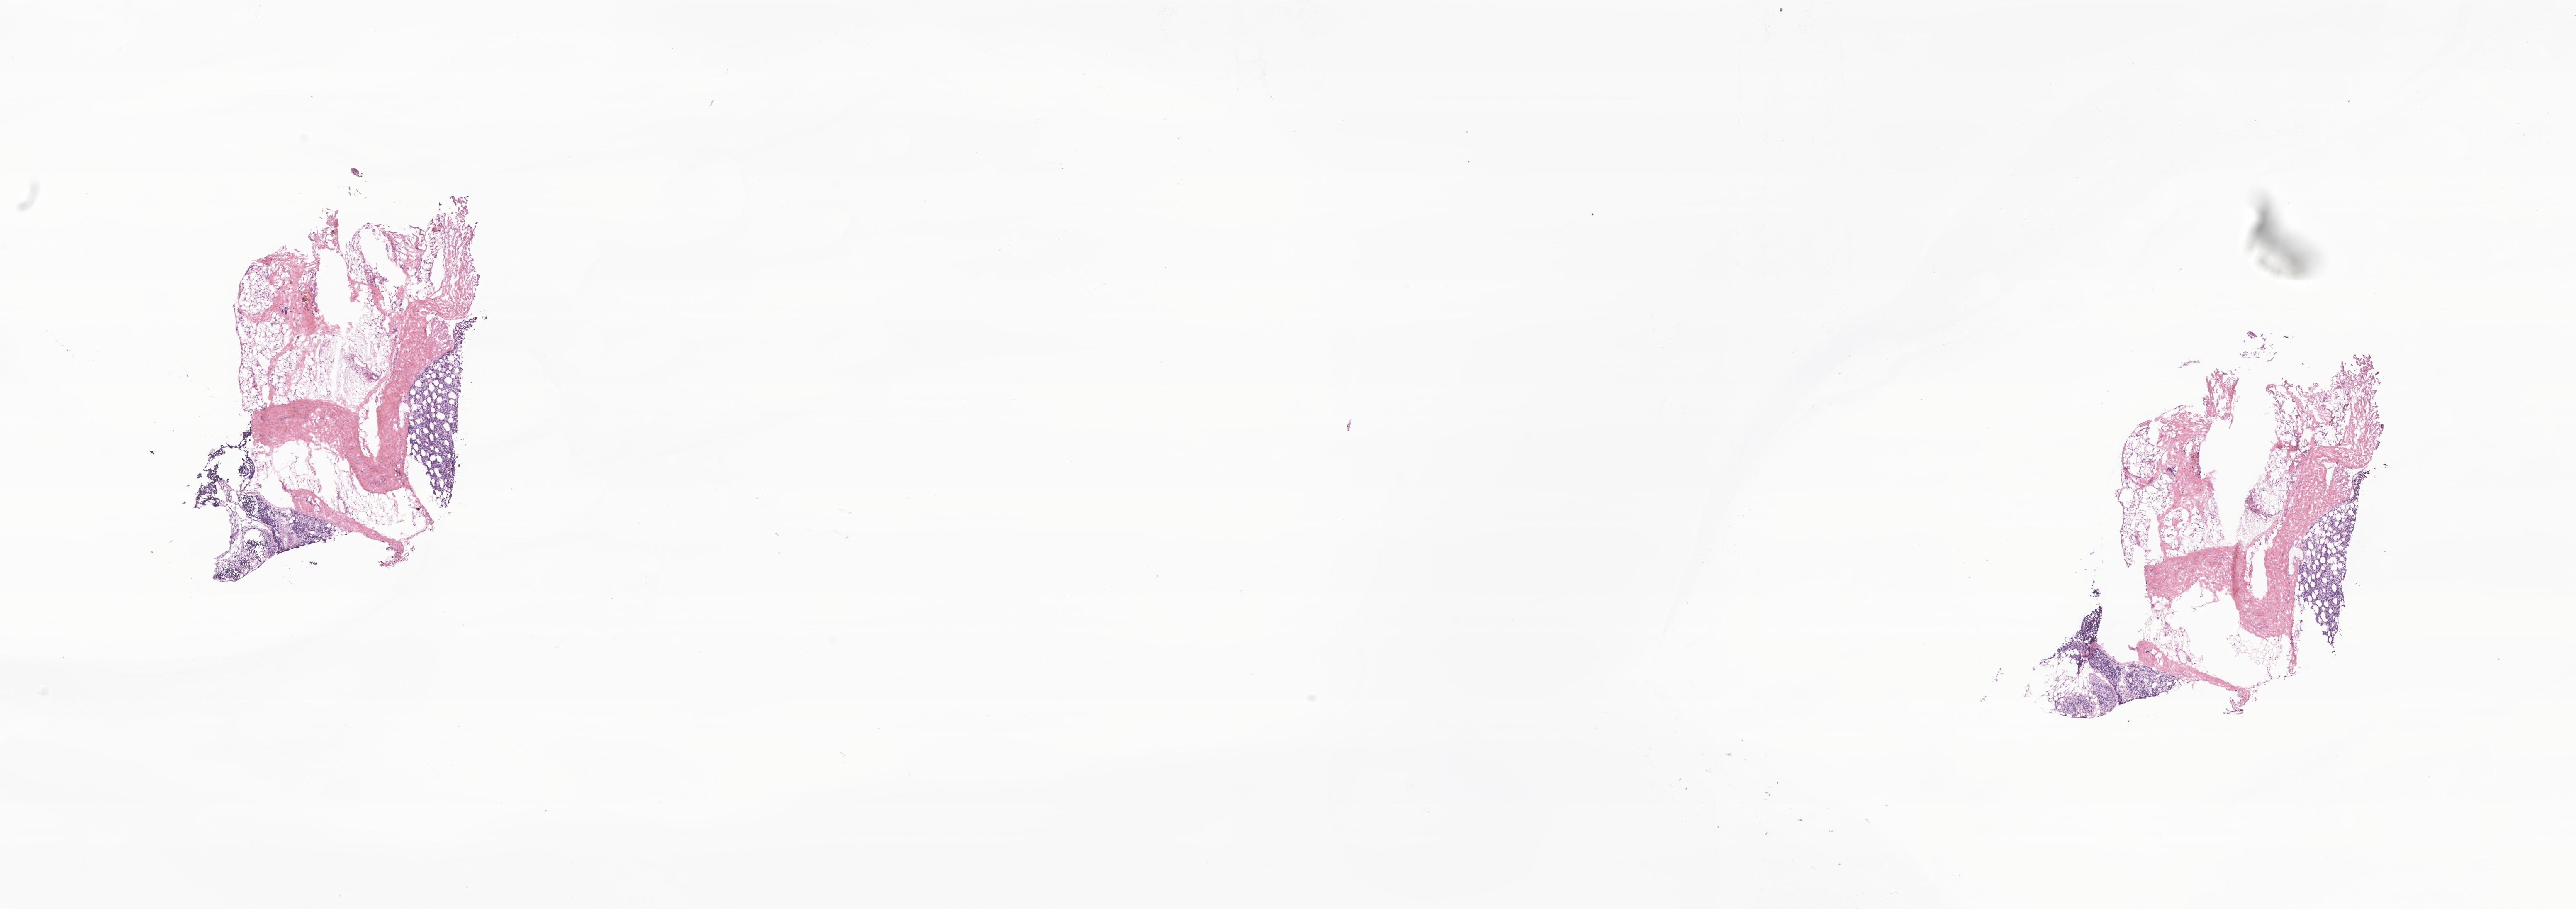
Whole-slide image, haematoxylin and eosin stain of tumor tissue from the abdomen — a low-resolution overview of the entire scanned area, about 26.2 x 9.2 mm. Frozen section. Male patient, age 153 days.
Diagnosis: Neuroblastoma, NOS.